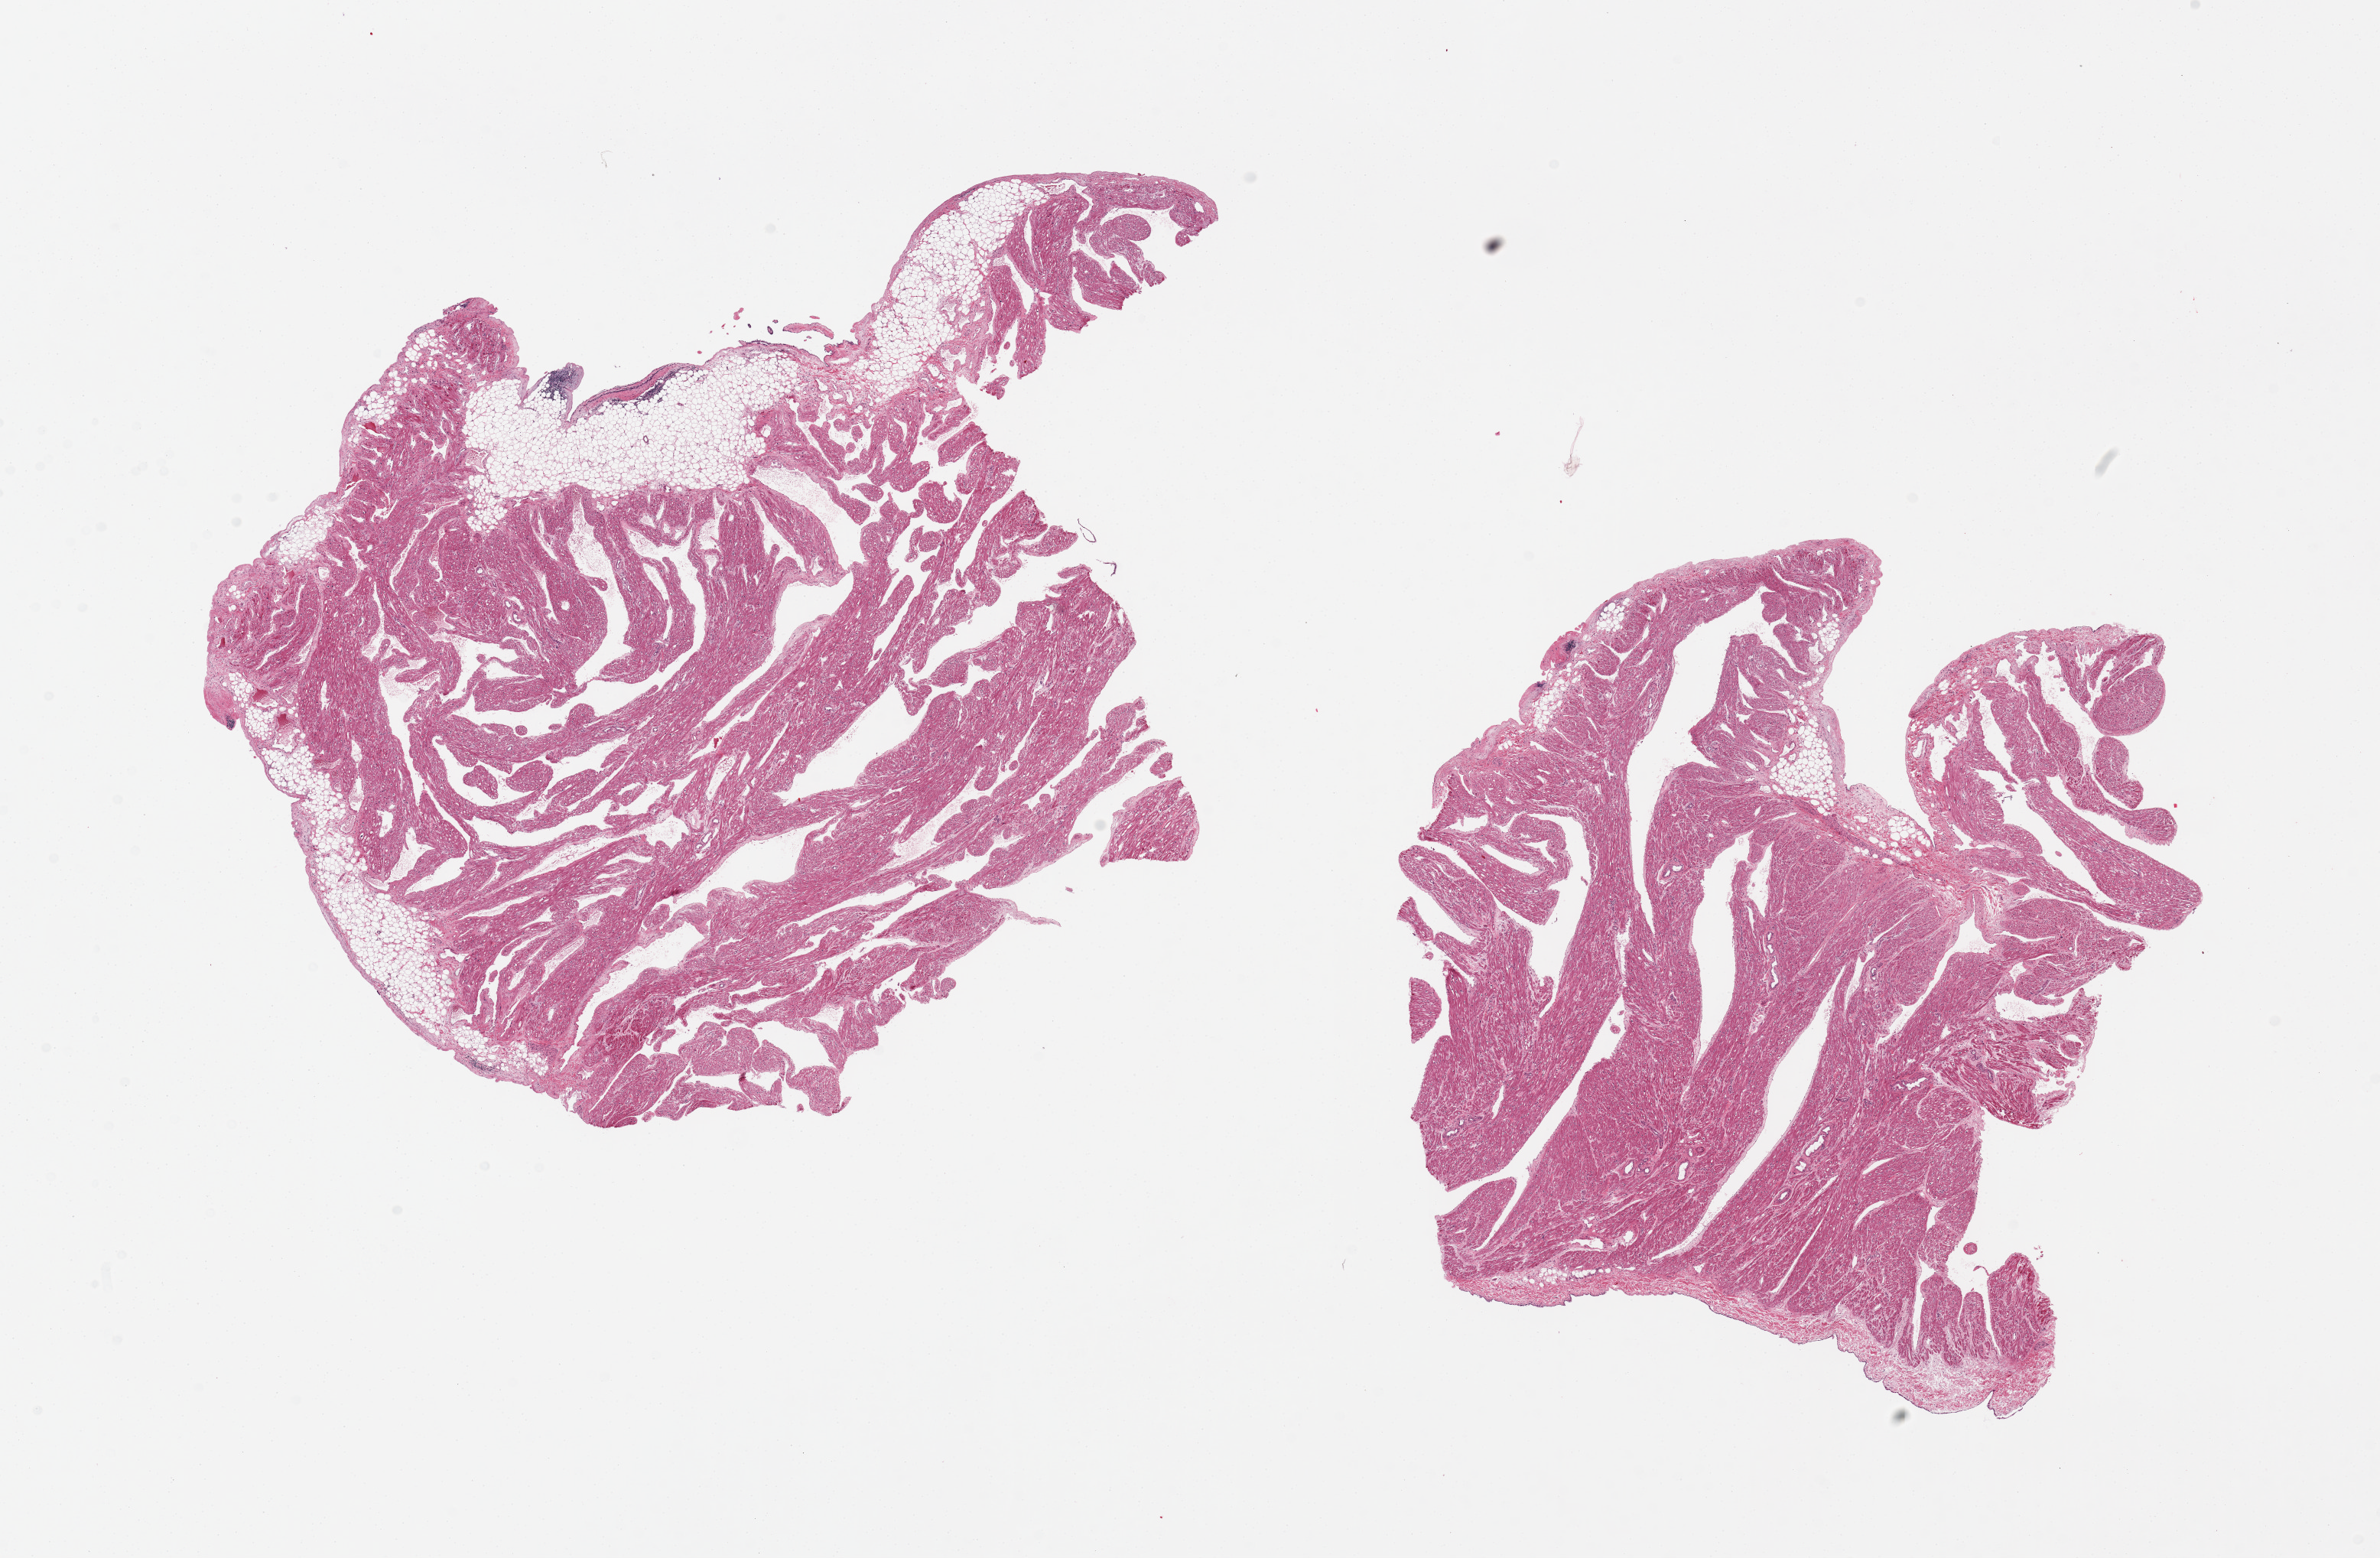
H&E whole-slide image, whole scanned area (about 24.6 x 16.1 mm) shown as a low-resolution overview, PAXgene-fixed paraffin-embedded (PFPE) section, section of auricular appendage (target tissue), tissue donor sample. Donor: male.
Review note (as recorded): 2 pieces; one approximately 10% adipose tissue, the other with scant adipose tissue. Few collections of chronic inflammatory cells.